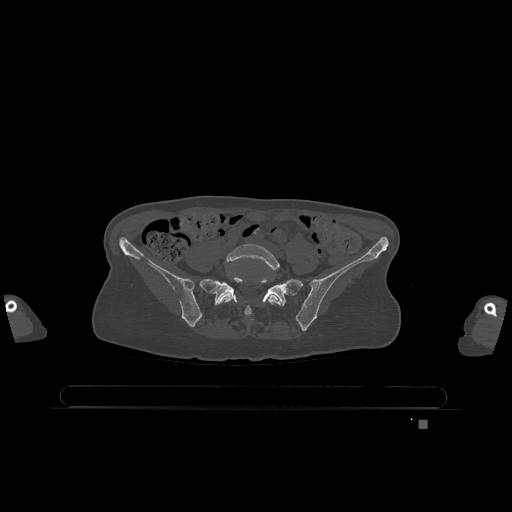
CT including the spine, one axial slice. Bone window (W 1800 / L 400 HU). 0.5 mm slice thickness. 512 × 512 image matrix. Female patient, age 74 years. Case-level facts recorded for this patient, not image findings: primary cancer: lung; vertebrae with lytic lesions (as recorded): T1, T4, T5, T6, L4, L5.
Structures marked on this image (semi-automatic segmentation, software-assisted and operator-edited):
- L5 vertebra: bounding box (x1, y1, x2, y2) in pixels: (217, 244, 282, 316)